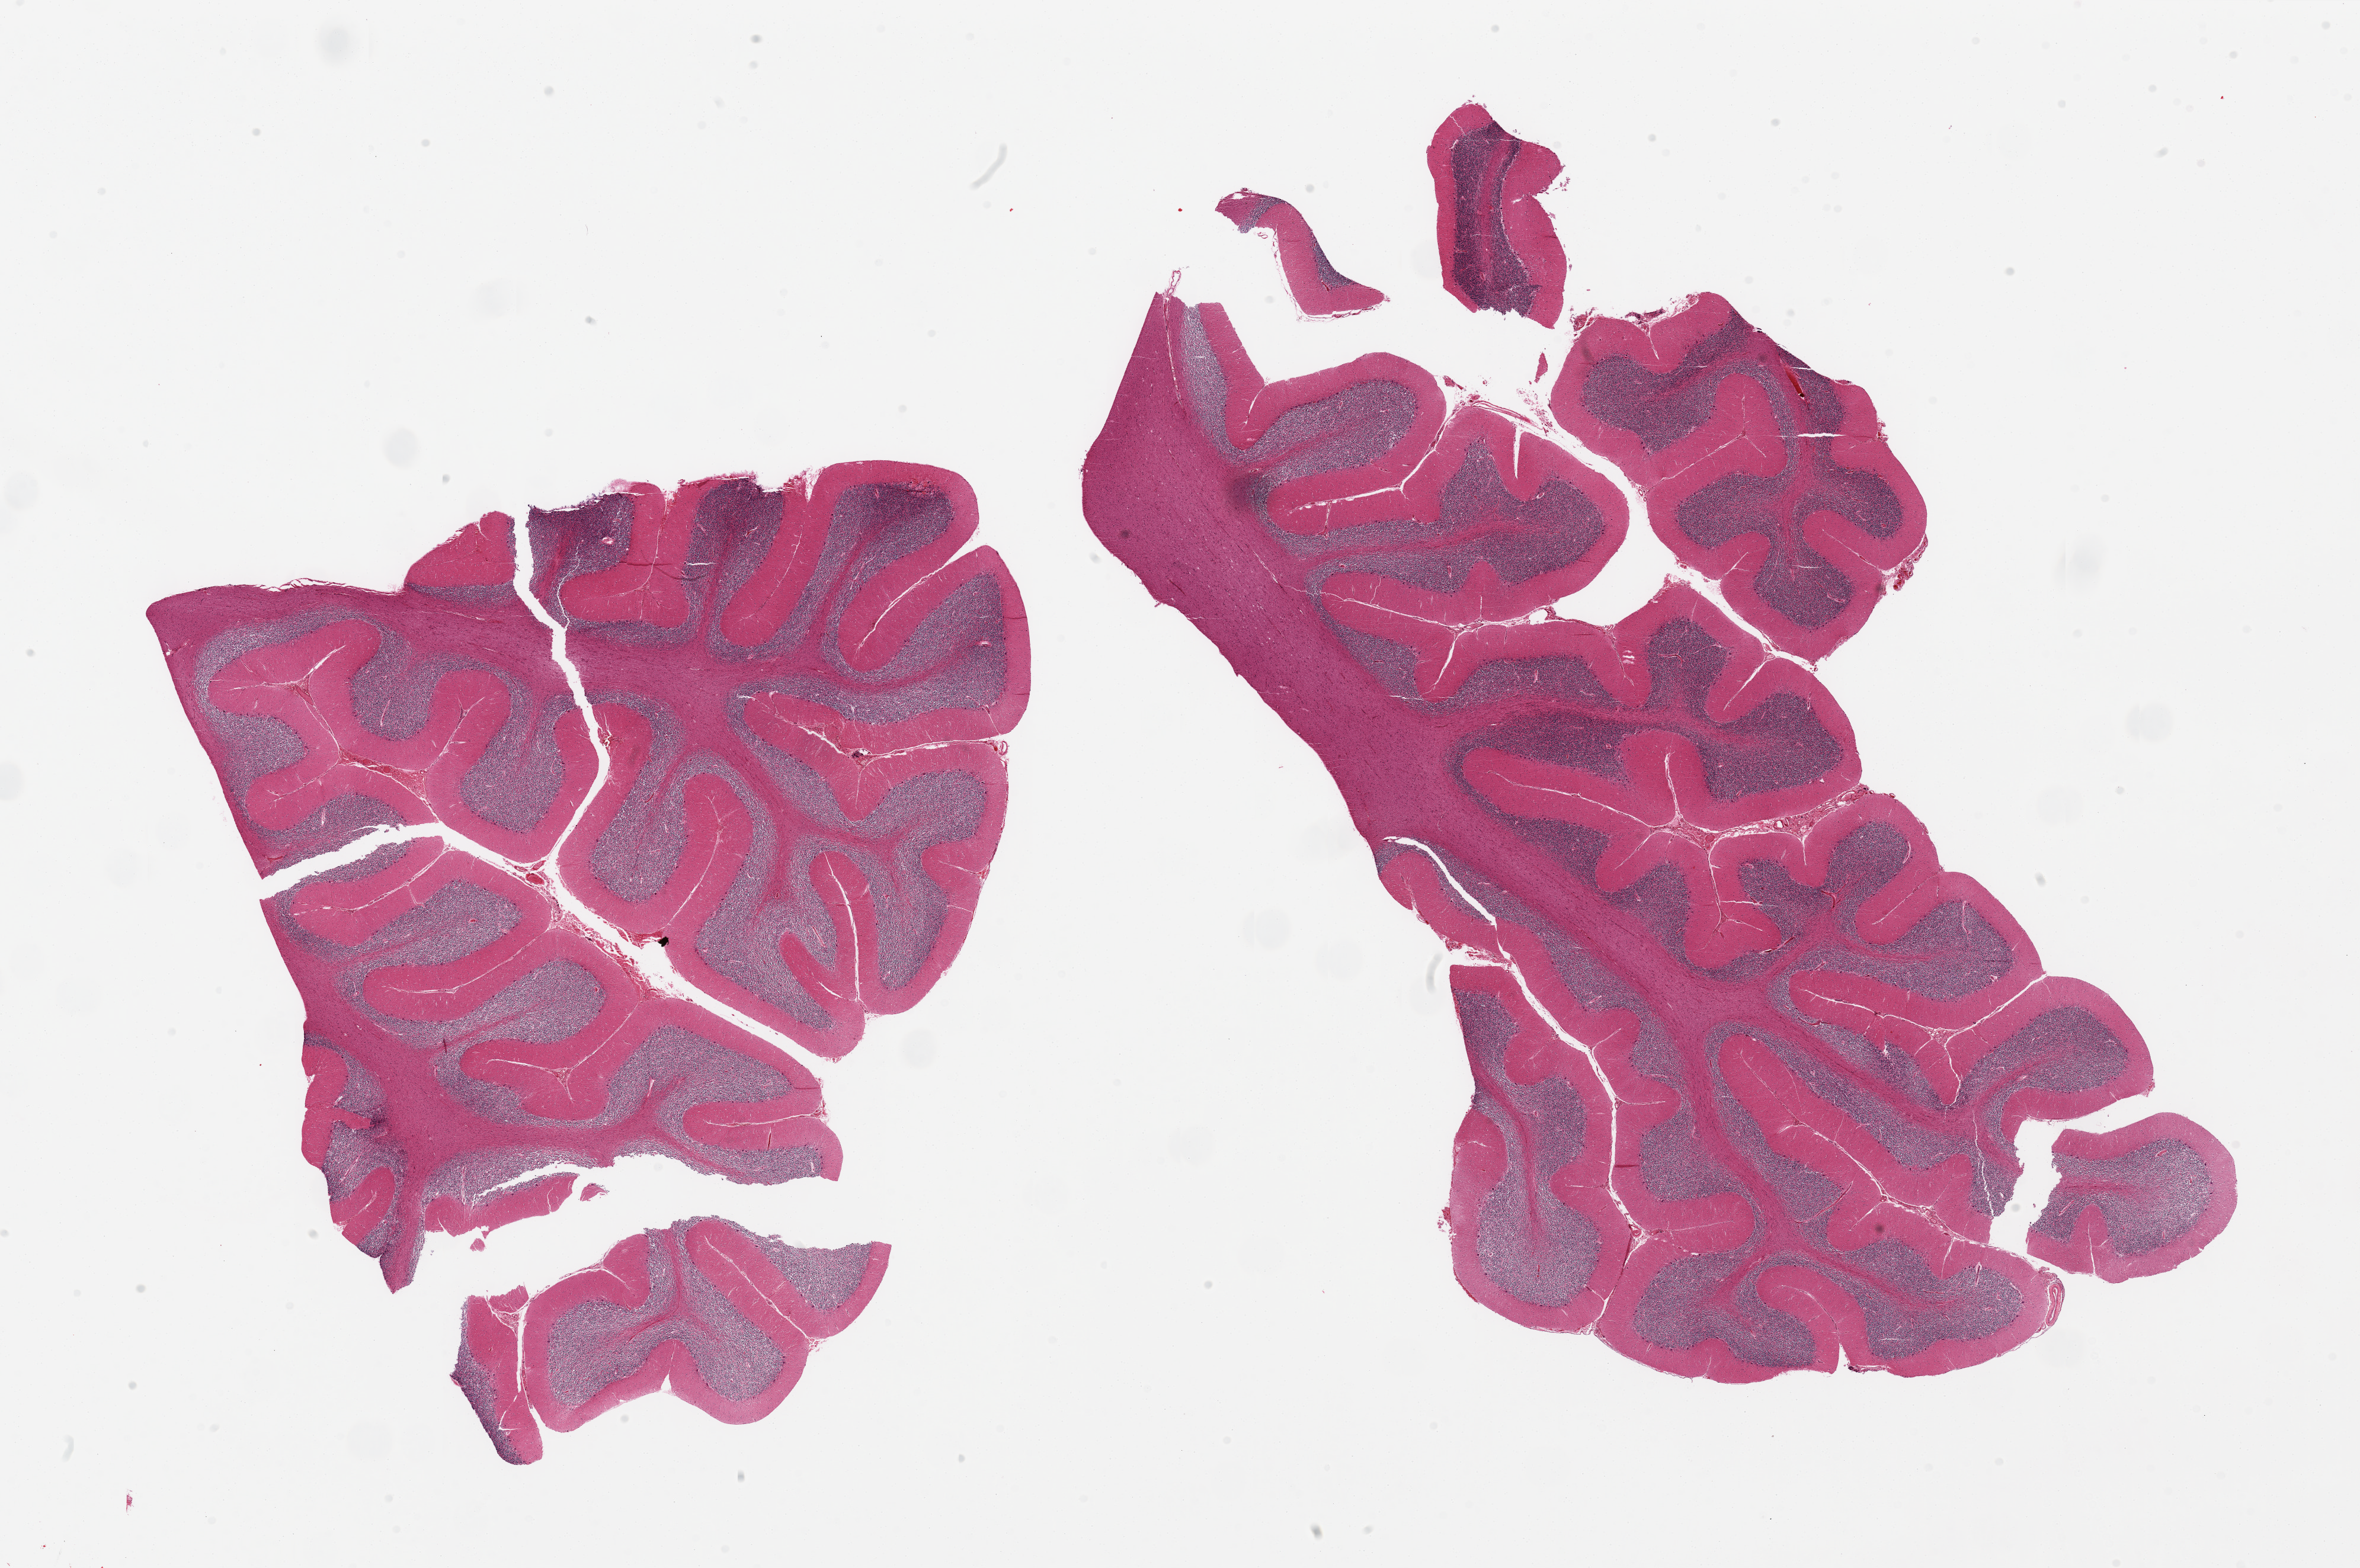
Whole-slide image, hematoxylin and eosin (H&E) stain, a low-resolution overview of the entire scanned area, about 31.5 x 20.9 mm (from a 20x scan); PAXgene-fixed, paraffin-embedded tissue; sampled site (target tissue): cerebellum; tissue donor sample. Donor: female.
• reviewer comment on this tissue sample: 2 pieces, fragmented